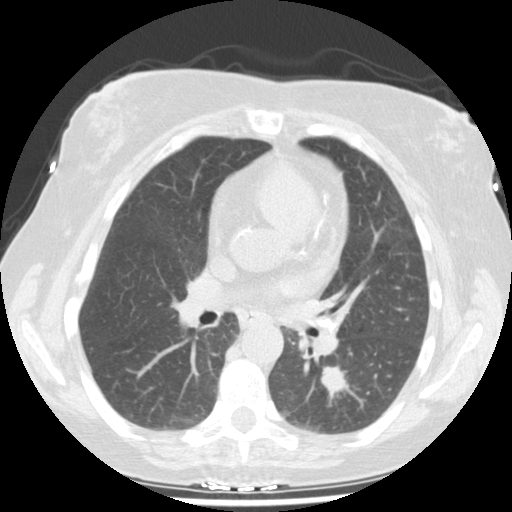
Axial slice from a low-dose chest CT screening exam. Second screening round (one year after baseline). Lung window (W 1500 / L -600 HU). 2.5 mm slice thickness. Standard (soft-tissue) reconstruction kernel (STANDARD). Slice 66 of 159 in the series. Female participant, aged 61 years at enrolment. Current smoker at enrolment.
• Expert-annotated lung lesion, bounding box <312,354,364,406> (left, top, right, bottom; pixels).
• The screening reader recorded 2 non-calcified nodules or masses ≥4 mm on this exam (left lower lobe, right upper lobe); which of them this box marks is not recorded.
• Official screen result: positive, change unspecified: nodule(s) >= 4 mm or enlarging nodule(s), mass(es), or other non-specific abnormalities suspicious for lung cancer.
• Lung cancer was diagnosed 69 days after this screen: squamous cell carcinoma, NOS, left lower lobe, moderately differentiated (G2), stage IA (AJCC 6th edition), 12 mm at pathology.